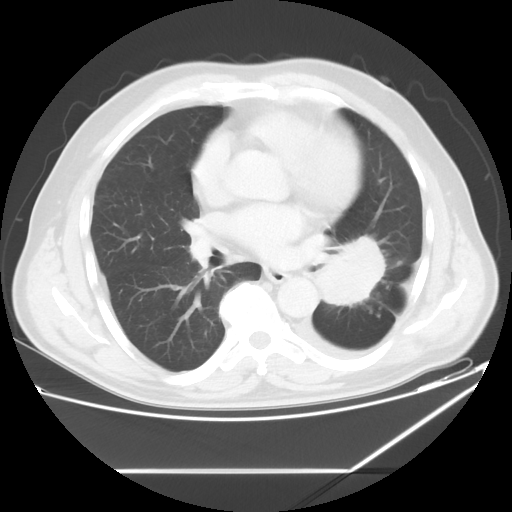
Chest CT, one axial slice; position 30 of 60 along the scan axis; reconstruction kernel STANDARD; lung window (W 1500 / L -600 HU); 512 × 512 image matrix, field of view 395 × 395 mm. Male patient, age 62 years. From the clinical record (not read from this slice): clinical TNM (as recorded): T3 N0 M1.
Structures marked on this image (bounding box drawn by a radiologist):
- lung tumour (recorded histology: adenocarcinoma): bounding box [x1, y1, x2, y2] px = [314, 236, 388, 308]
- lung tumour (recorded histology: adenocarcinoma): [319, 233, 392, 308]